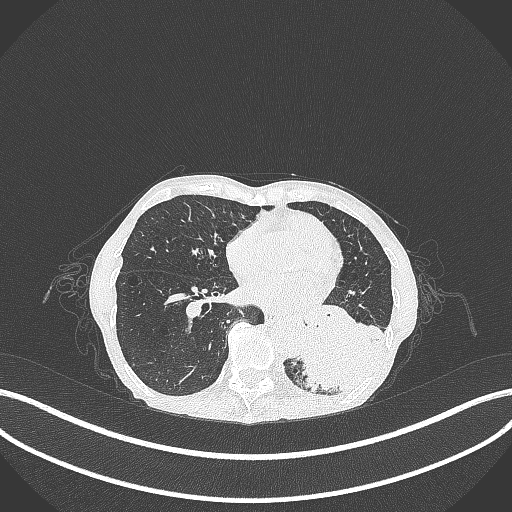
Chest CT, one axial slice; slice 101 of 347 in the series (ordered by position); reconstruction kernel B70f; 120 kVp; lung window (W 1500 / L -600 HU); 1 mm slice thickness; 512 × 512 image matrix, field of view 400 × 400 mm. Patient: female, 70 years. Case-level facts recorded for this patient, not image findings: clinical TNM (as recorded): T3 N0 M0; histopathological grade: G3.
Outlined on this slice (rectangle marked by the reading radiologist):
- lung tumour (recorded histology: small cell carcinoma): bounding box <297,316,388,396> (left, top, right, bottom; pixels)